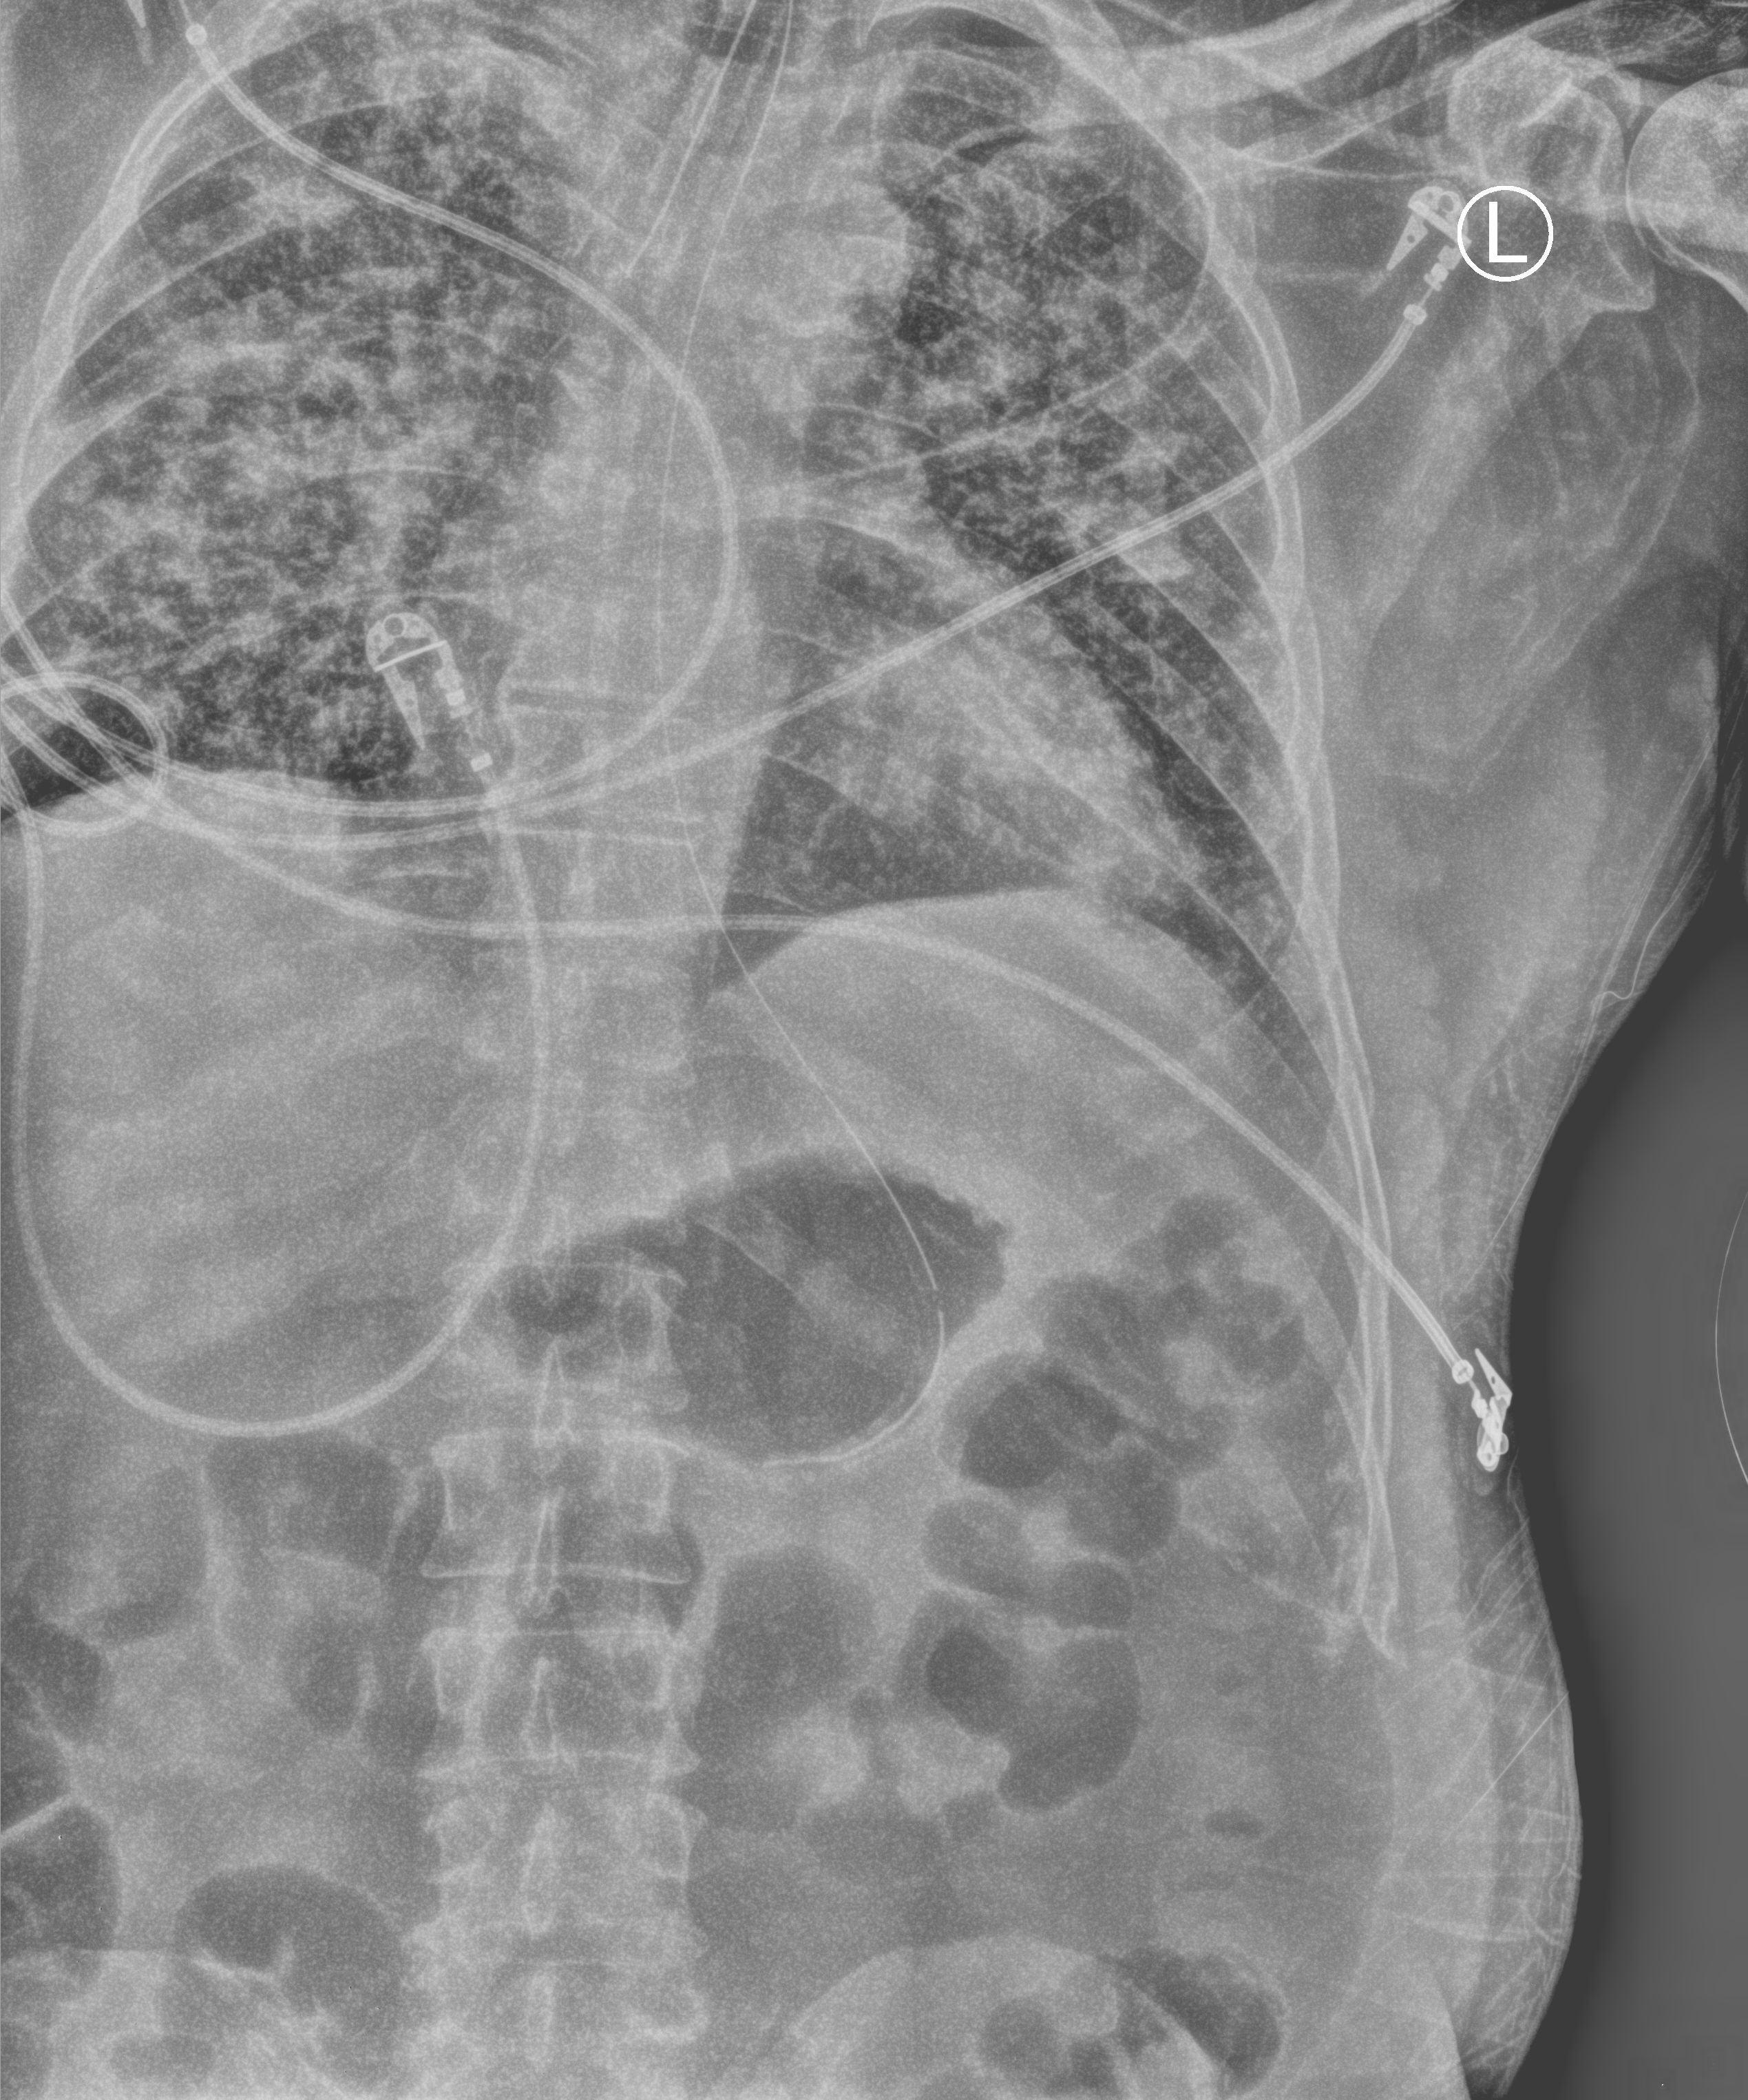
Chest X-ray (portable), anteroposterior (AP) projection. Male patient hospitalised with COVID-19, age 18–59 years.
Admission-level facts for this patient (not findings on this image; timing relative to this image not recorded):
- mechanically ventilated during this hospital stay: yes